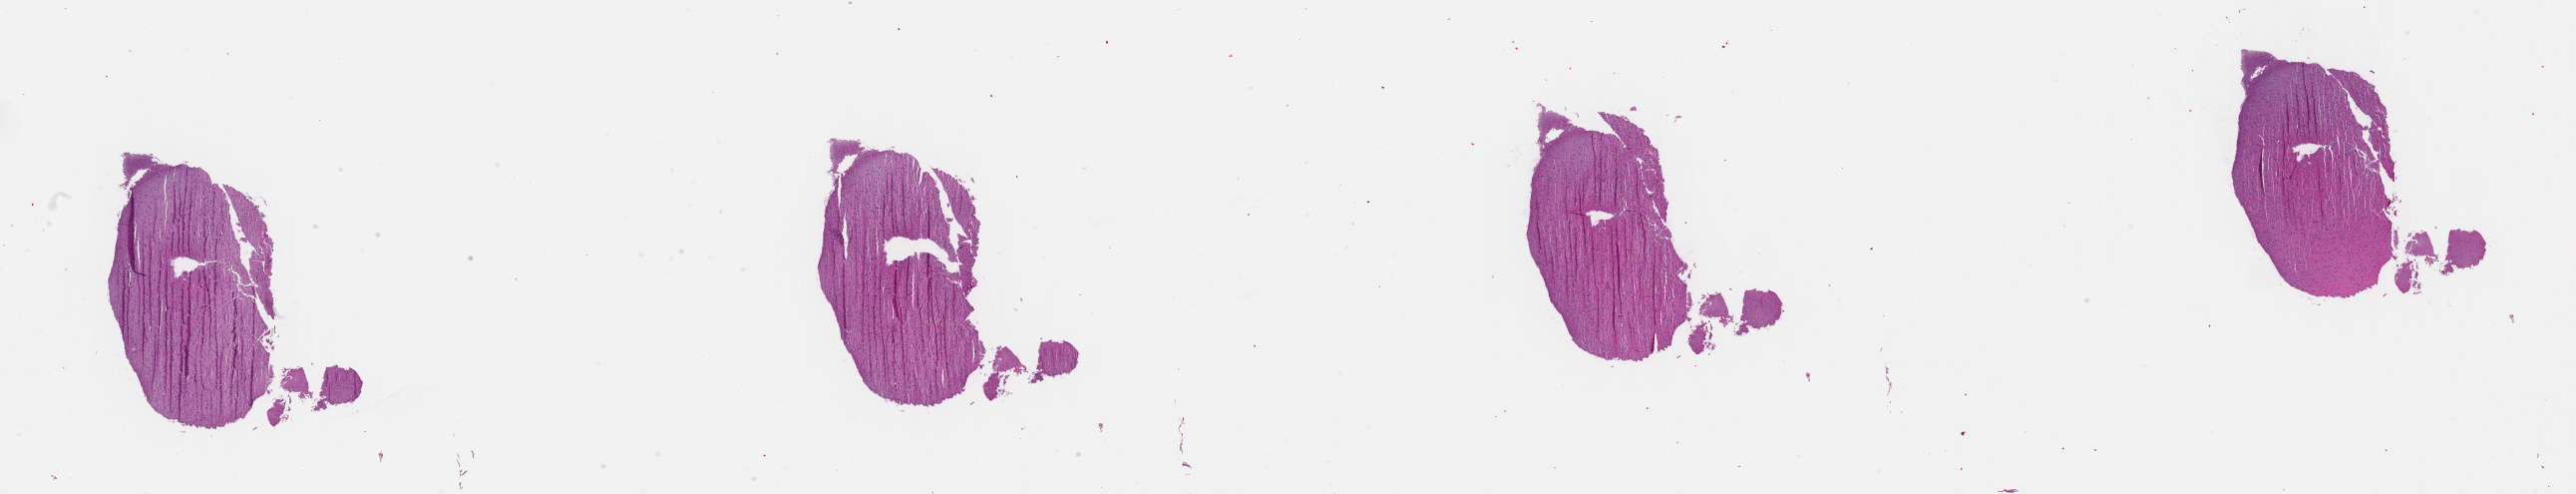
Digitized H&E-stained tissue section (whole slide) — low-resolution overview of the scanned area, about 41.8 x 8.0 mm. Formalin-fixed paraffin-embedded (FFPE) diagnostic section. Brain, primary tumour sample. Female patient; age at initial diagnosis 74 years. Histologic grade: G2 (moderately differentiated).
* diagnosis: Mixed glioma (cerebrum)